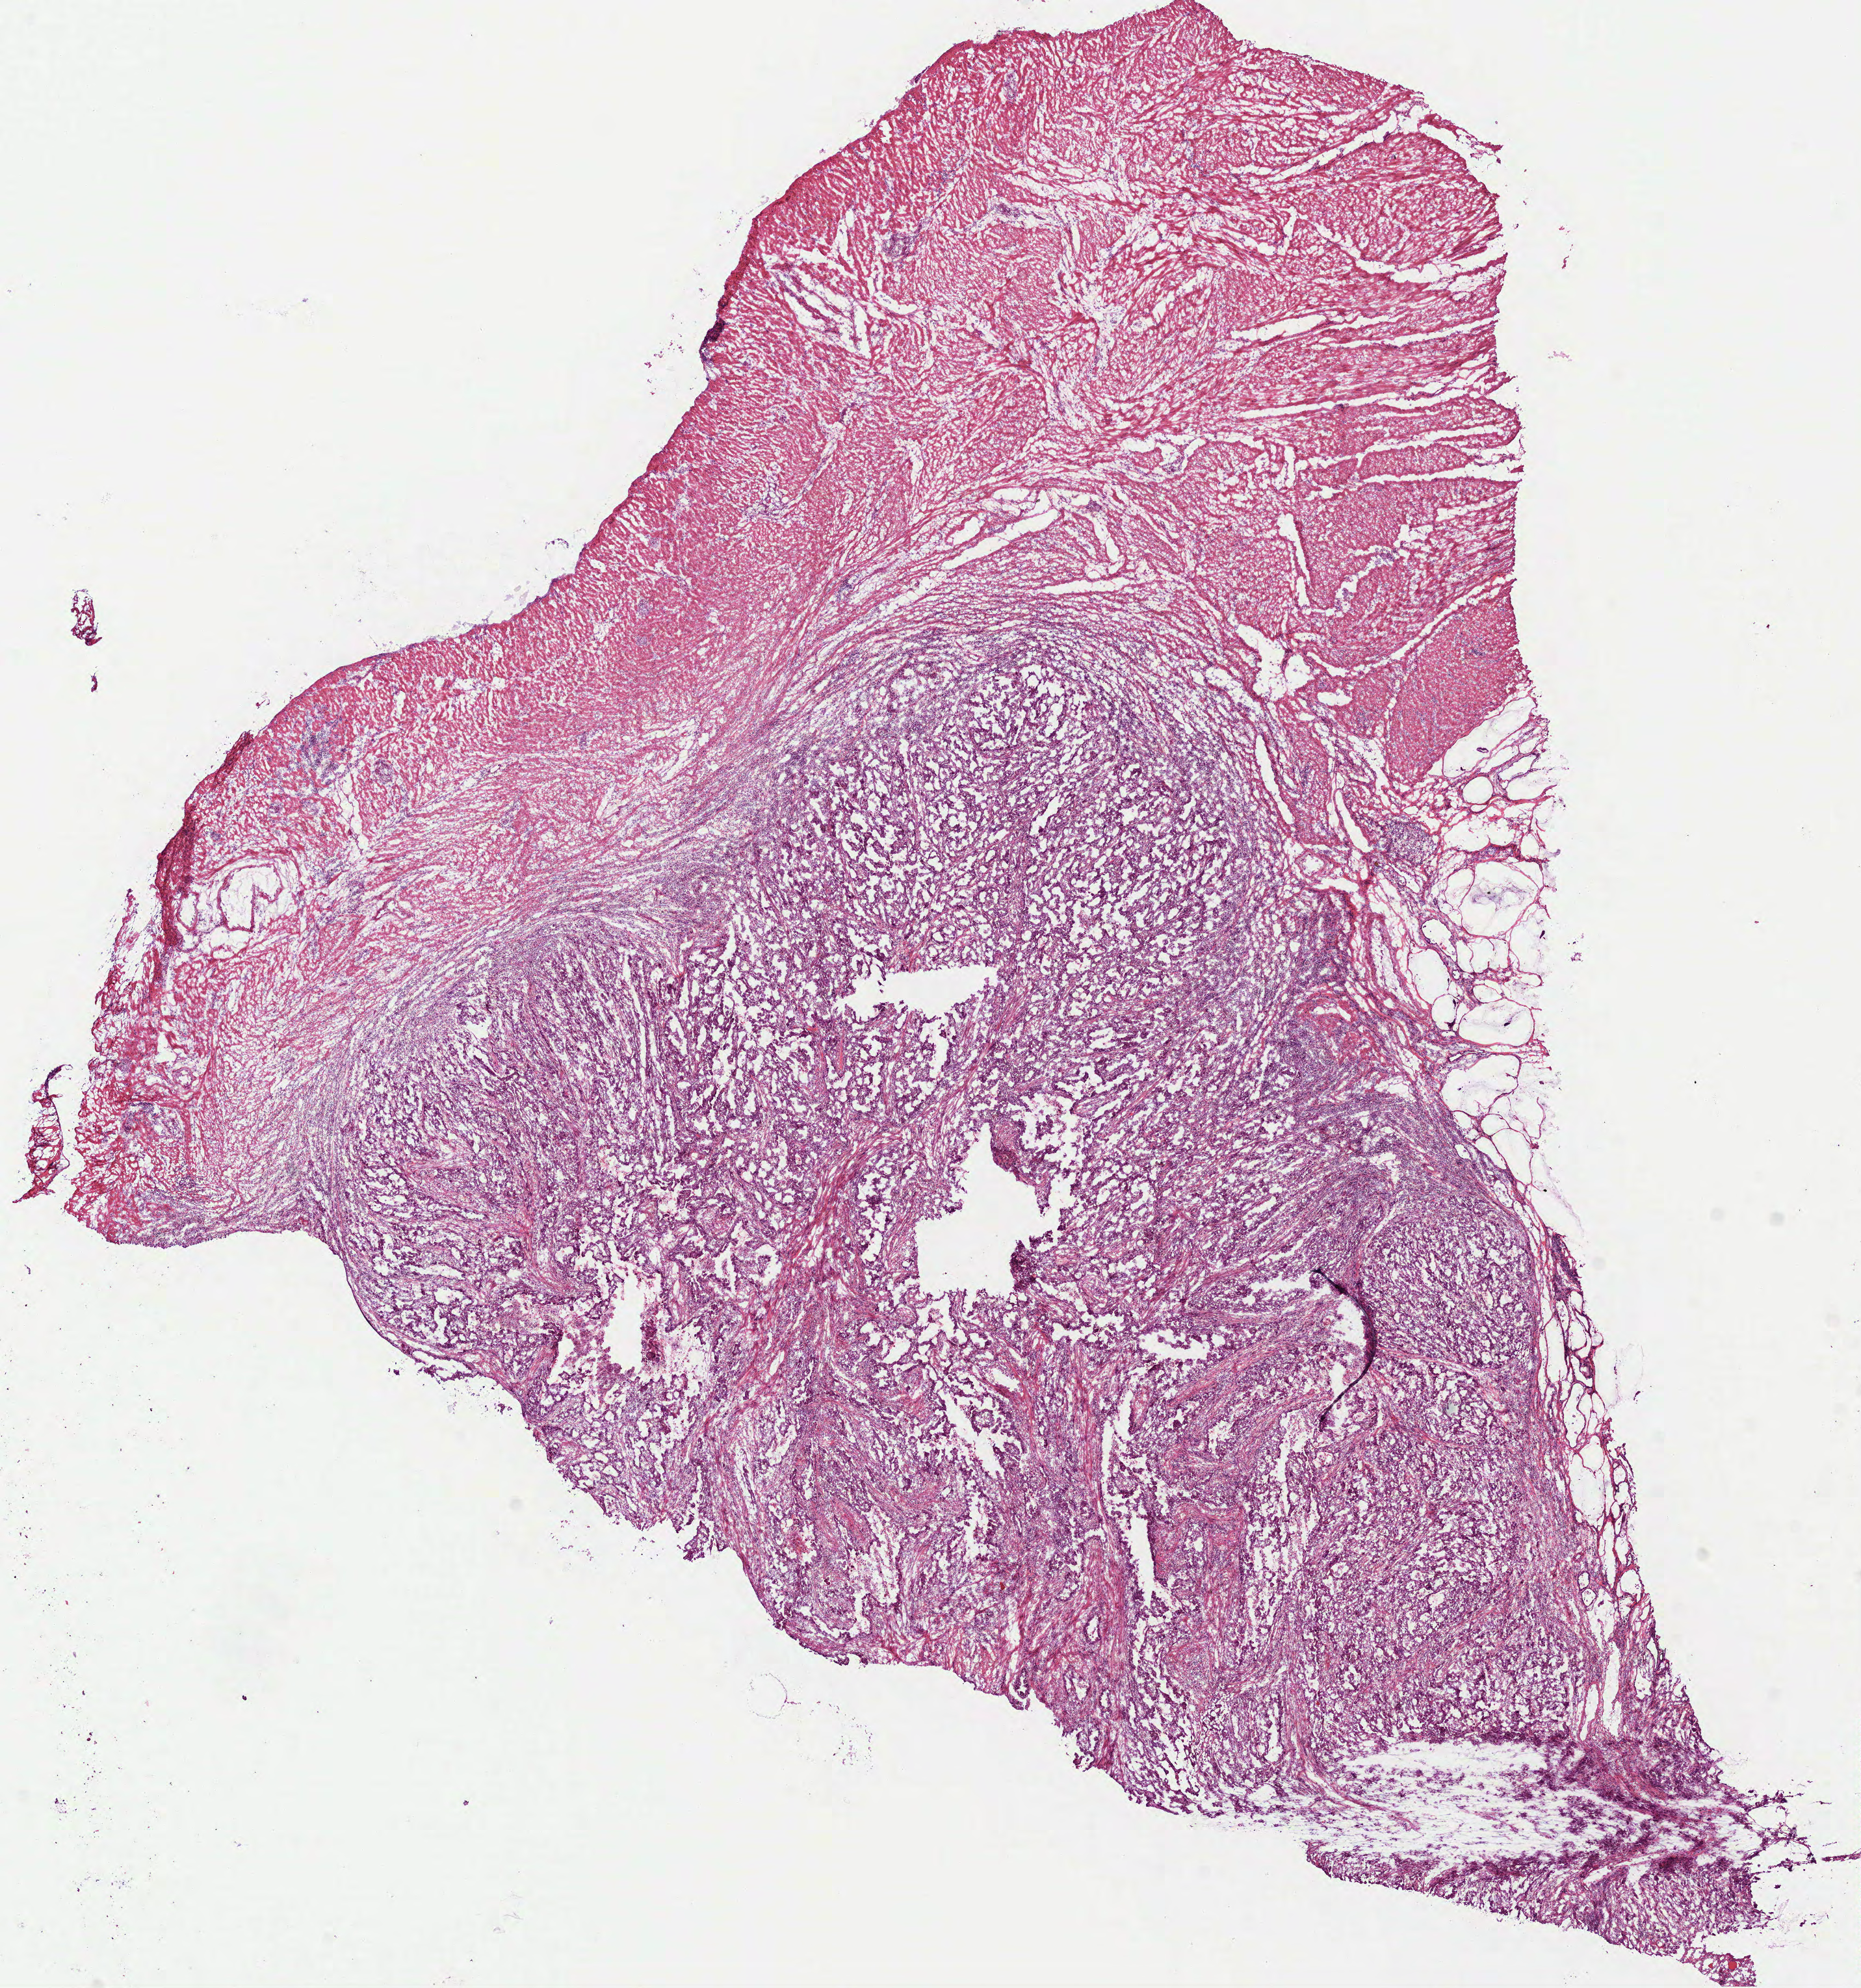
Digitized H&E tissue section (whole slide) — shown as a low-resolution overview of the whole scanned area (about 11.5 x 12.3 mm, from a 40x scan); frozen section from the bottom of the tissue portion; sample: primary tumour, stomach. Female patient; age at initial diagnosis 82 years. Histologic grade: G3 (poorly differentiated). Slide review estimates, as recorded: tumour cells 75%, tumour nuclei 60%, normal cells 0%, stromal cells 25%, necrosis 0%.
• AJCC pathologic stage: IIIA (6th edition)
• lymph nodes positive (case pathology): 2 of 2 examined
• pathologic diagnosis: Mucinous adenocarcinoma (gastric antrum)